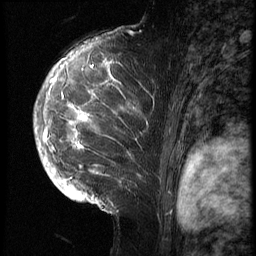
Breast MRI (dynamic contrast-enhanced), one sagittal slice; position 44 of 70 along the scan axis; 3 images stored at this slice position (order not interpretable as contrast timing); 1.5 T; TE 4.2 ms, TR 9 ms; 2.5 mm slice thickness; 256 × 256 image matrix, field of view 180 × 180 mm. Female patient, age 28 years. Case-level facts recorded for this patient, not image findings: setting: breast cancer imaged before/during neoadjuvant chemotherapy.
Structures marked on this image (semi-automatic segmentation, software-assisted and operator-edited):
- analysis volume of interest (the breast-tissue region the enhancement analysis was run in; not a lesion): bounding box <43,42,159,215> (left, top, right, bottom; pixels)
- tumour enhancement mask (voxels above the 140 % enhancement threshold inside the analysis volume of interest): <44,54,137,200>